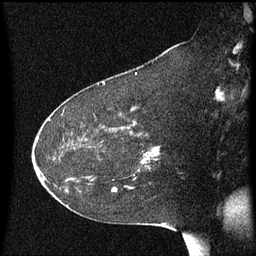
Breast MRI (dynamic contrast-enhanced), one sagittal slice. Position 35 of 60 along the scan axis. Dynamic contrast-enhanced series, image 2 of 3 at this slice position (ordered by acquisition). 1.5 T. TE 4.2 ms, TR 8.4 ms. 2 mm slice thickness. 256 × 256 image matrix, field of view 200 × 200 mm. Patient: female, 54 years. Case-level facts recorded for this patient, not image findings: setting: breast cancer imaged before/during neoadjuvant chemotherapy; receptor status: HR-positive, HER2-negative.
Annotated regions visible in this slice (semi-automatically segmented with operator editing):
- analysis volume of interest (the breast-tissue region the enhancement analysis was run in; not a lesion): bounding box [x1, y1, x2, y2] px = [117, 132, 161, 171]
- tumour enhancement mask (voxels above the 70 % enhancement threshold inside the analysis volume of interest): [143, 148, 157, 163]